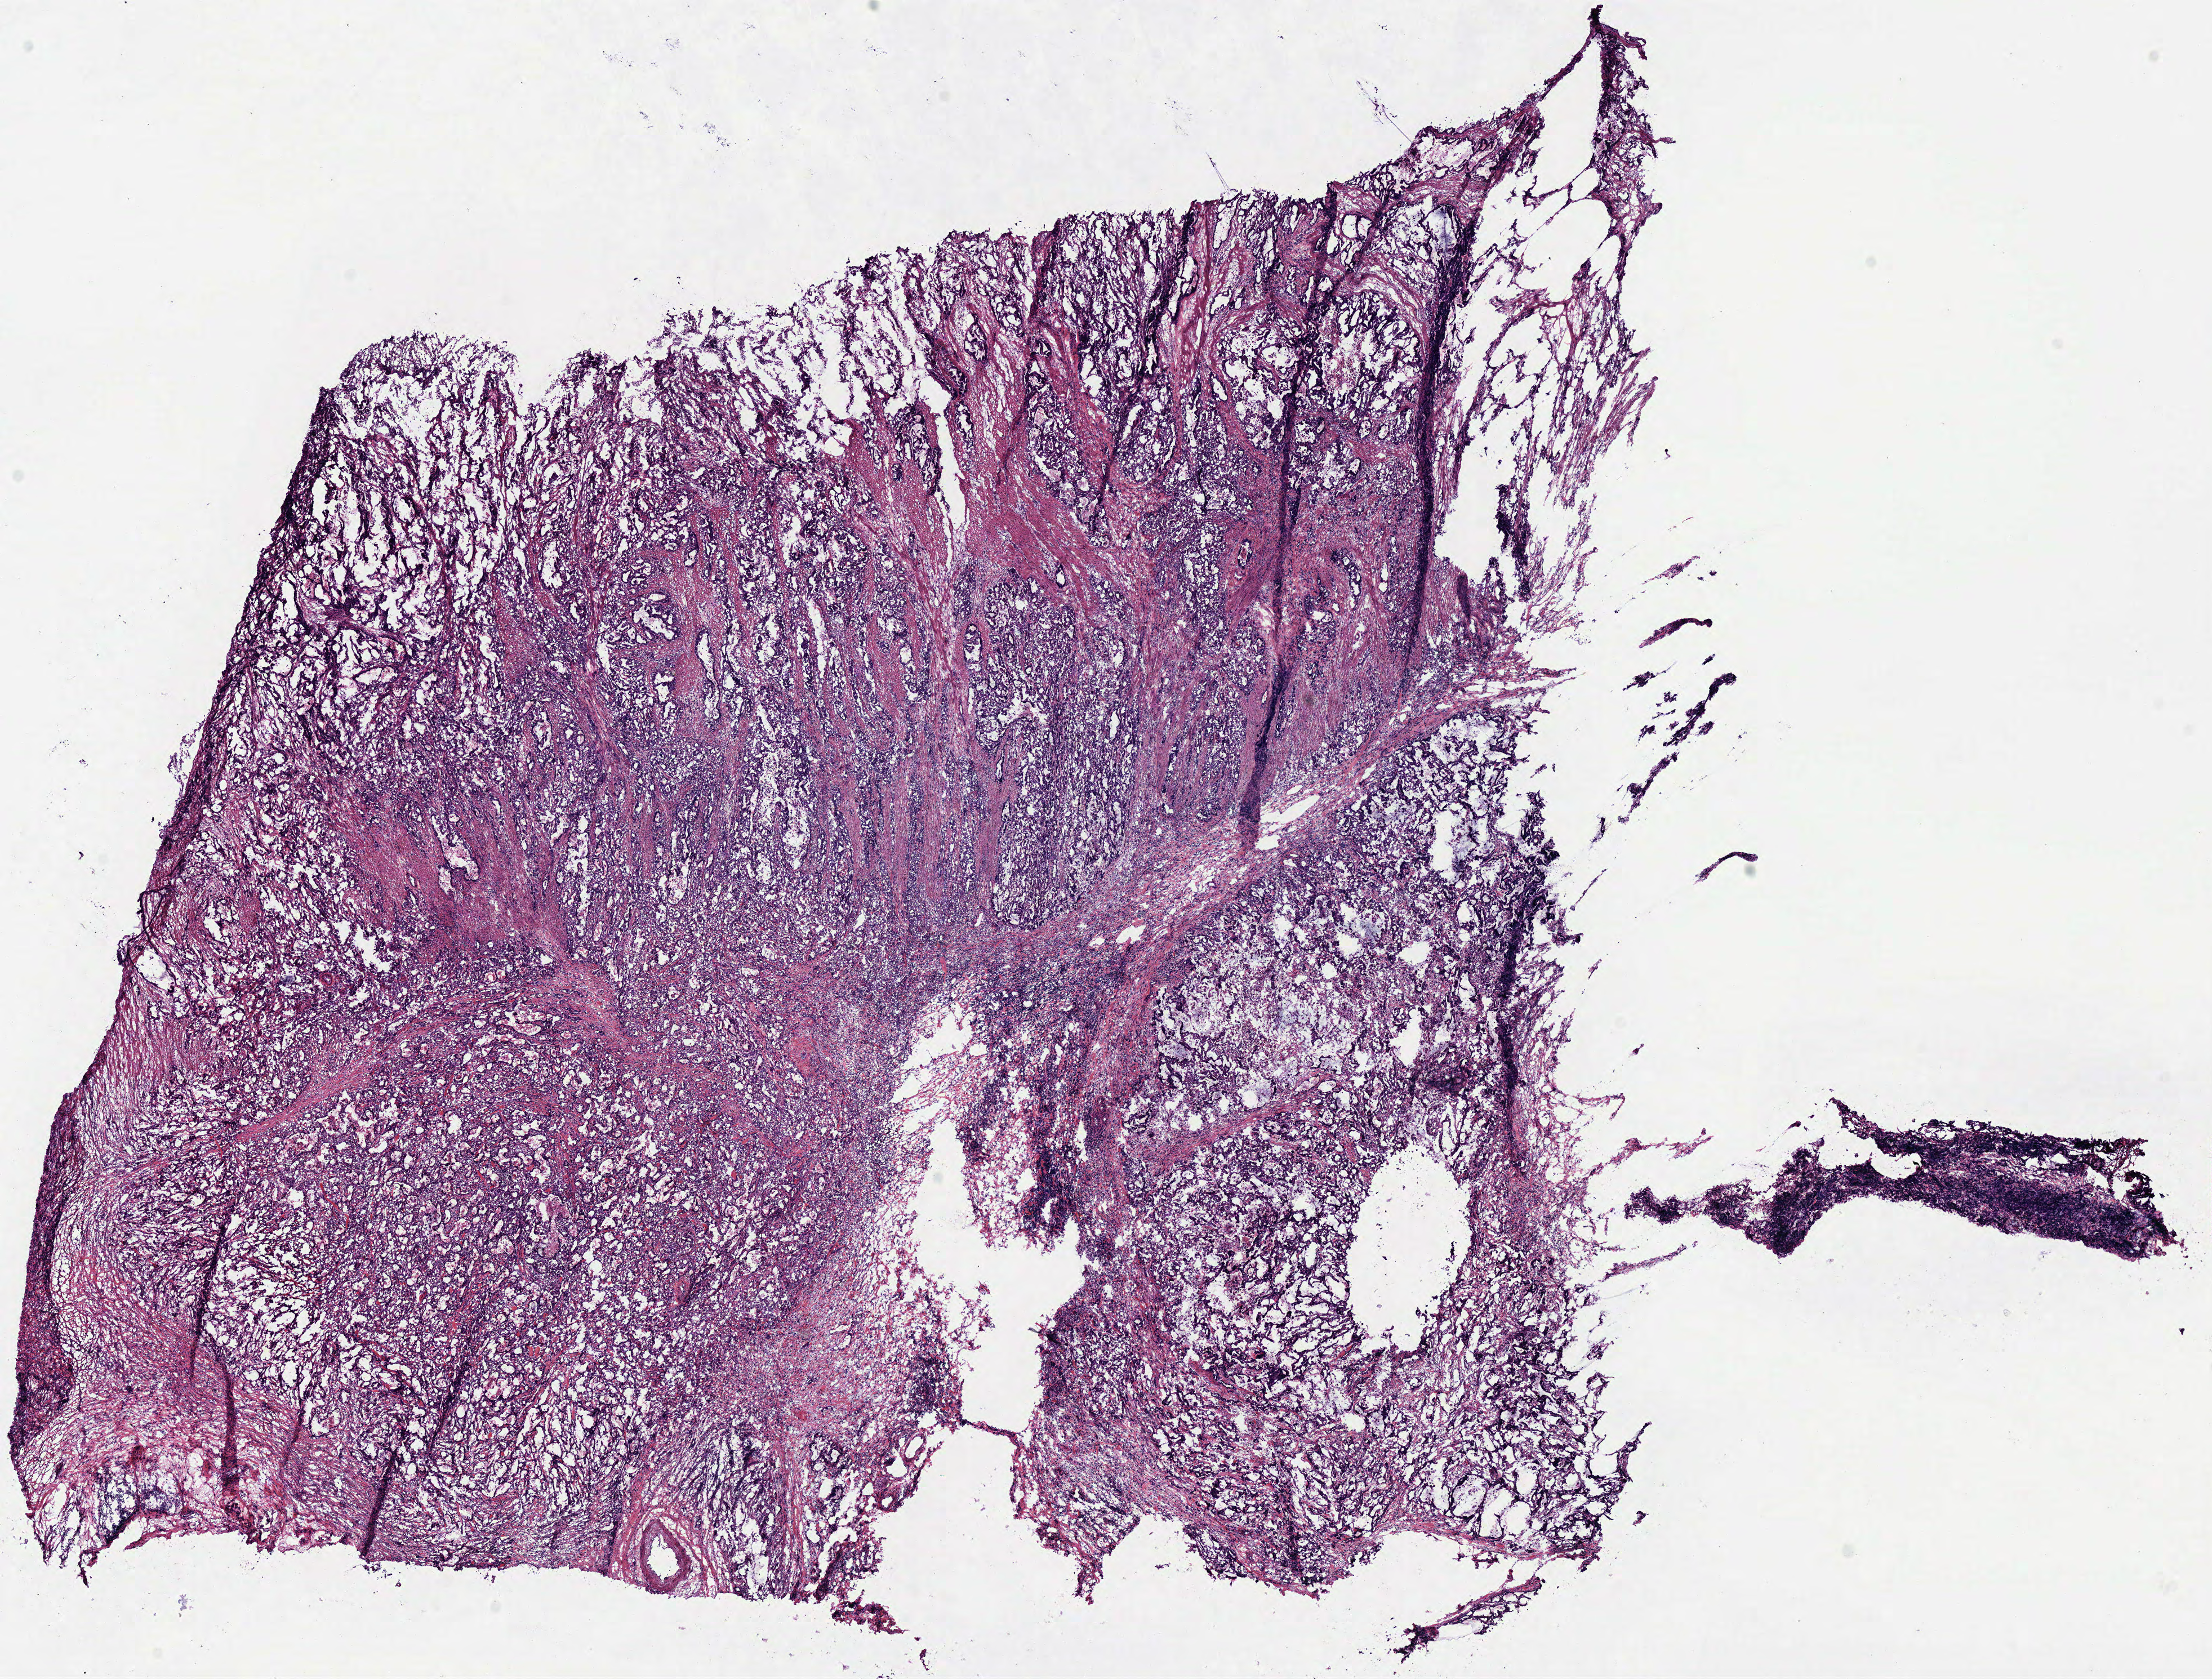
Digitized H&E tissue section (whole slide) — shown as a low-resolution overview of the whole scanned area (about 15.5 x 11.7 mm, from a 40x scan), frozen section, sample: primary tumour, stomach. Male patient. Histologic grade: G2 (moderately differentiated). Pathologist review of this section (percent, as recorded): tumour cells 85%, tumour nuclei 75%, normal cells 0%, stromal cells 15%, necrosis 0%.
- pathologic diagnosis: Adenocarcinoma, NOS (cardia, NOS)